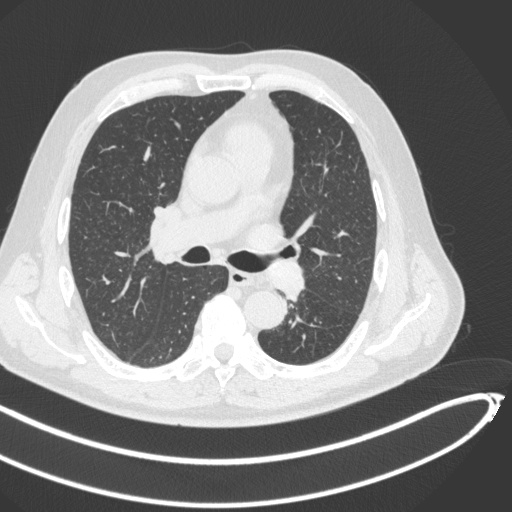
Chest CT, one axial slice; slice 273 of 466 in the series (ordered by position); lung window (W 1500 / L -600 HU); 1 mm slice thickness; 512 × 512 image matrix, field of view 400 × 400 mm. Male patient, age 64 years. Case-level facts recorded for this patient, not image findings: clinical TNM (as recorded): T1c N0 M0; histopathological grade: G2.
Annotated regions visible in this slice (rectangle marked by the reading radiologist):
- lung tumour (recorded histology: squamous cell carcinoma): box from (x=269, y=262) to (x=306, y=301) px